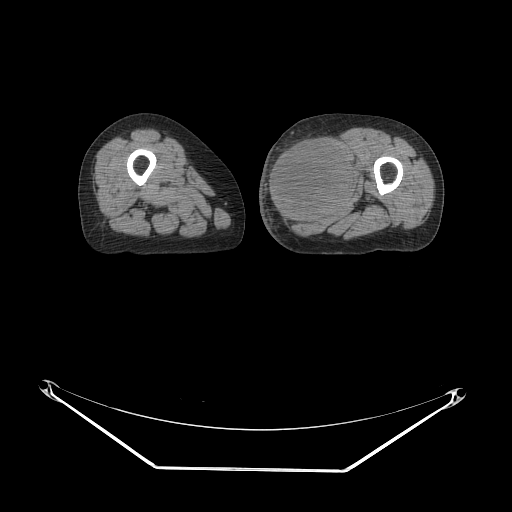
CT of an extremity soft-tissue mass (from a PET/CT study), one axial slice. Position 28 of 91 along the scan axis. Soft-tissue window (W 400 / L 40 HU). 3.75 mm slice thickness. 512 × 512 image matrix. Female patient. From the clinical record (not read from this slice): histological type: pleomorphic leiomyosarcoma; grade: high; site of the primary tumour: left thigh.
Annotated regions visible in this slice (expert contour drawn on MRI and transferred to this co-registered scan by the dataset authors):
- gross tumour volume including surrounding oedema: box from (x=267, y=133) to (x=357, y=225) px
- gross tumour volume (mass): (x=267, y=133)–(x=355, y=222)